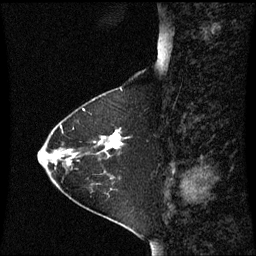
Breast MRI (dynamic contrast-enhanced), one sagittal slice. Dynamic contrast-enhanced series, image 2 of 3 at this slice position (ordered by acquisition). 1.5 T. TE 4.2 ms, TR 8.9 ms. 2 mm slice thickness. 256 × 256 image matrix, field of view 210 × 210 mm. Patient: female, 63 years. From the clinical record (not read from this slice): setting: breast cancer imaged before/during neoadjuvant chemotherapy; receptor status: HR-positive, HER2-negative.
Structures marked on this image (semi-automatic segmentation, software-assisted and operator-edited):
- analysis volume of interest (the breast-tissue region the enhancement analysis was run in; not a lesion): bounding box [x1, y1, x2, y2] px = [88, 131, 123, 161]
- tumour enhancement mask (voxels above the 70 % enhancement threshold inside the analysis volume of interest): [99, 132, 123, 150]